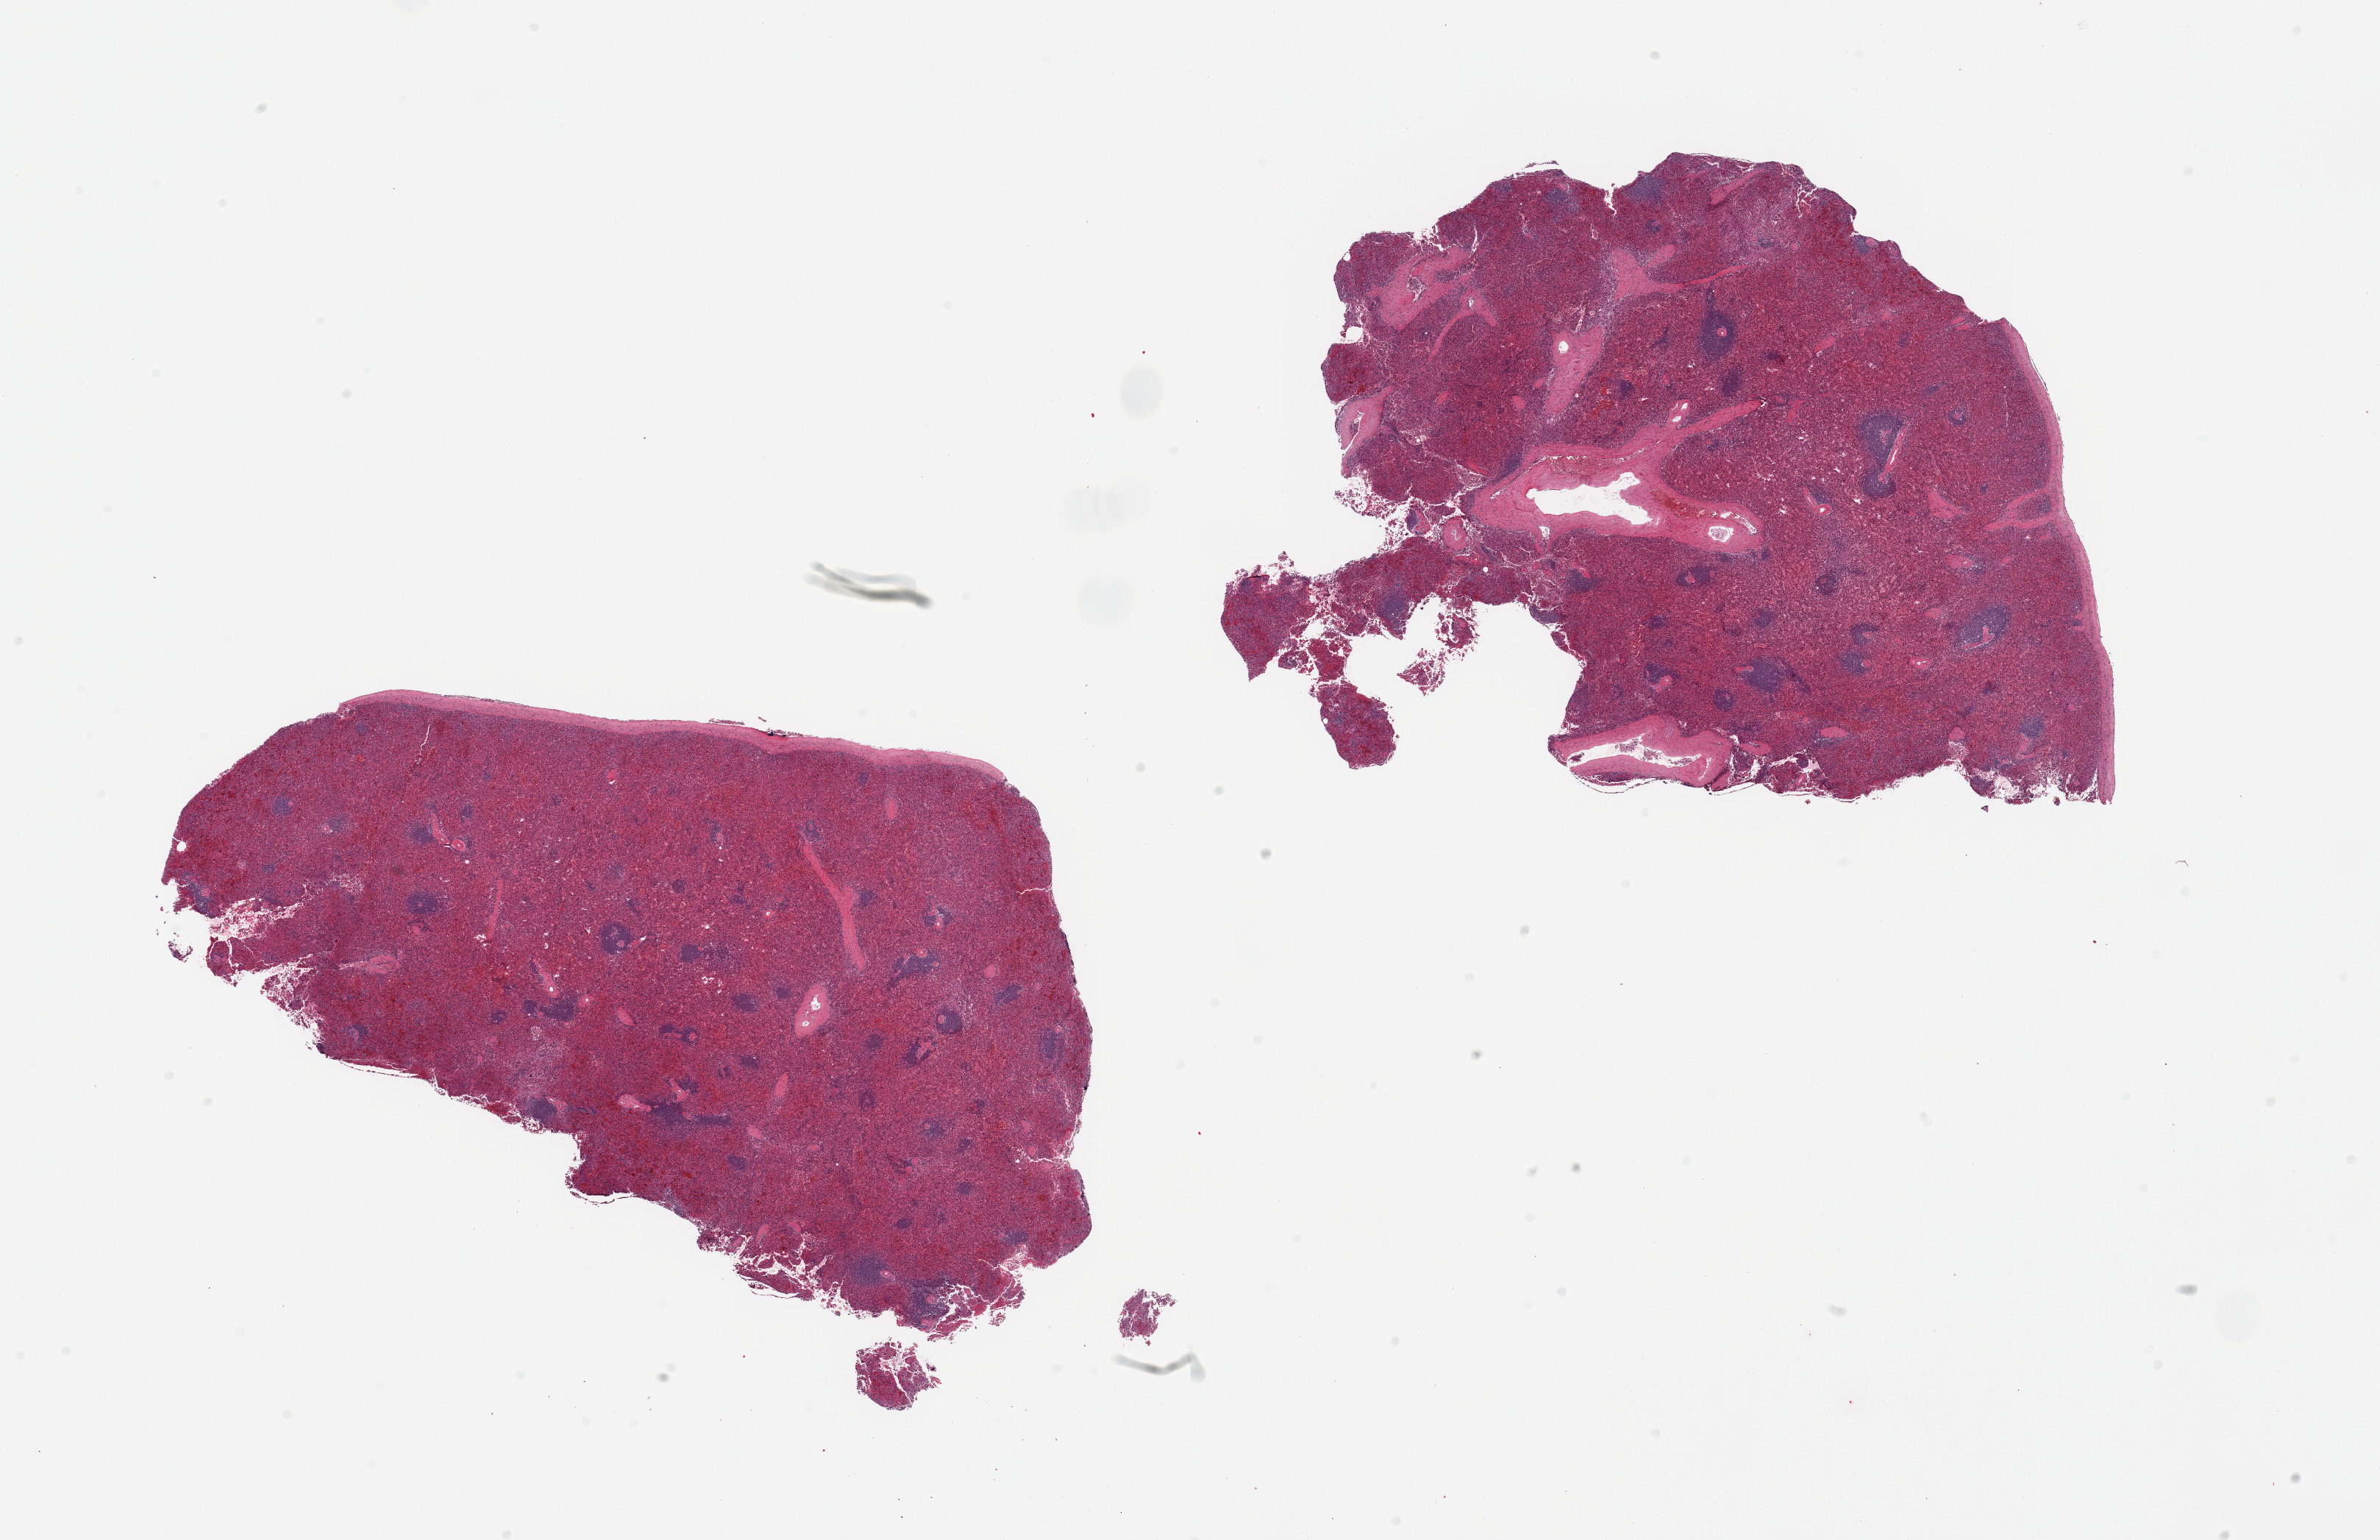
Haematoxylin and eosin whole-slide image — low-resolution overview of the scanned area, about 25.6 x 16.6 mm. PAXgene-fixed paraffin-embedded (PFPE) section. Sampled site (target tissue): spleen. Donor tissue sample. Donor sex: female.
Pathologist's review note for this sample: 2 pieces; capsule present.